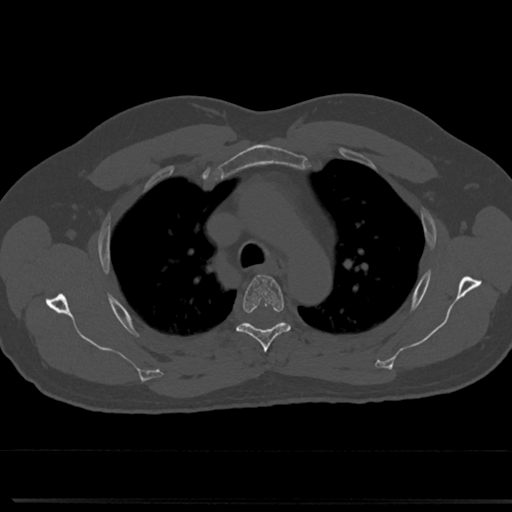
CT including the spine, one axial slice; reconstruction kernel Br40s/3; 120 kVp; bone window (W 1800 / L 400 HU); 0.5 mm slice thickness; 512 × 512 image matrix, field of view 355 × 355 mm. Patient: male, 61 years. Case-level facts recorded for this patient, not image findings: primary cancer: prostate.
Structures marked on this image (semi-automatic segmentation, software-assisted and operator-edited):
- T4 vertebra: bounding box (x1, y1, x2, y2) in pixels: (236, 275, 292, 351)
- T5 vertebra: (278, 322, 280, 324)